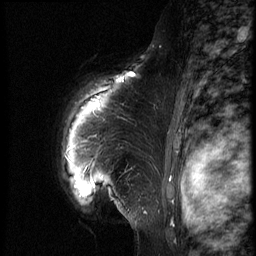
Breast MRI (dynamic contrast-enhanced), one sagittal slice. Slice 53 of 66 in the series (ordered by position). Dynamic contrast-enhanced series, image 2 of 3 at this slice position (ordered by acquisition). 1.5 T. TE 4.2 ms, TR 8.9 ms. 2.5 mm slice thickness. 256 × 256 image matrix, field of view 200 × 200 mm. Patient: female, 39 years. Case-level facts recorded for this patient, not image findings: setting: breast cancer imaged before/during neoadjuvant chemotherapy; receptor status: HER2-positive.
Annotated regions visible in this slice (semi-automatic segmentation, software-assisted and operator-edited):
- analysis volume of interest (the breast-tissue region the enhancement analysis was run in; not a lesion): bounding box <55,75,166,218> (left, top, right, bottom; pixels)
- tumour enhancement mask (voxels above the 140 % enhancement threshold inside the analysis volume of interest): <130,75,136,77>